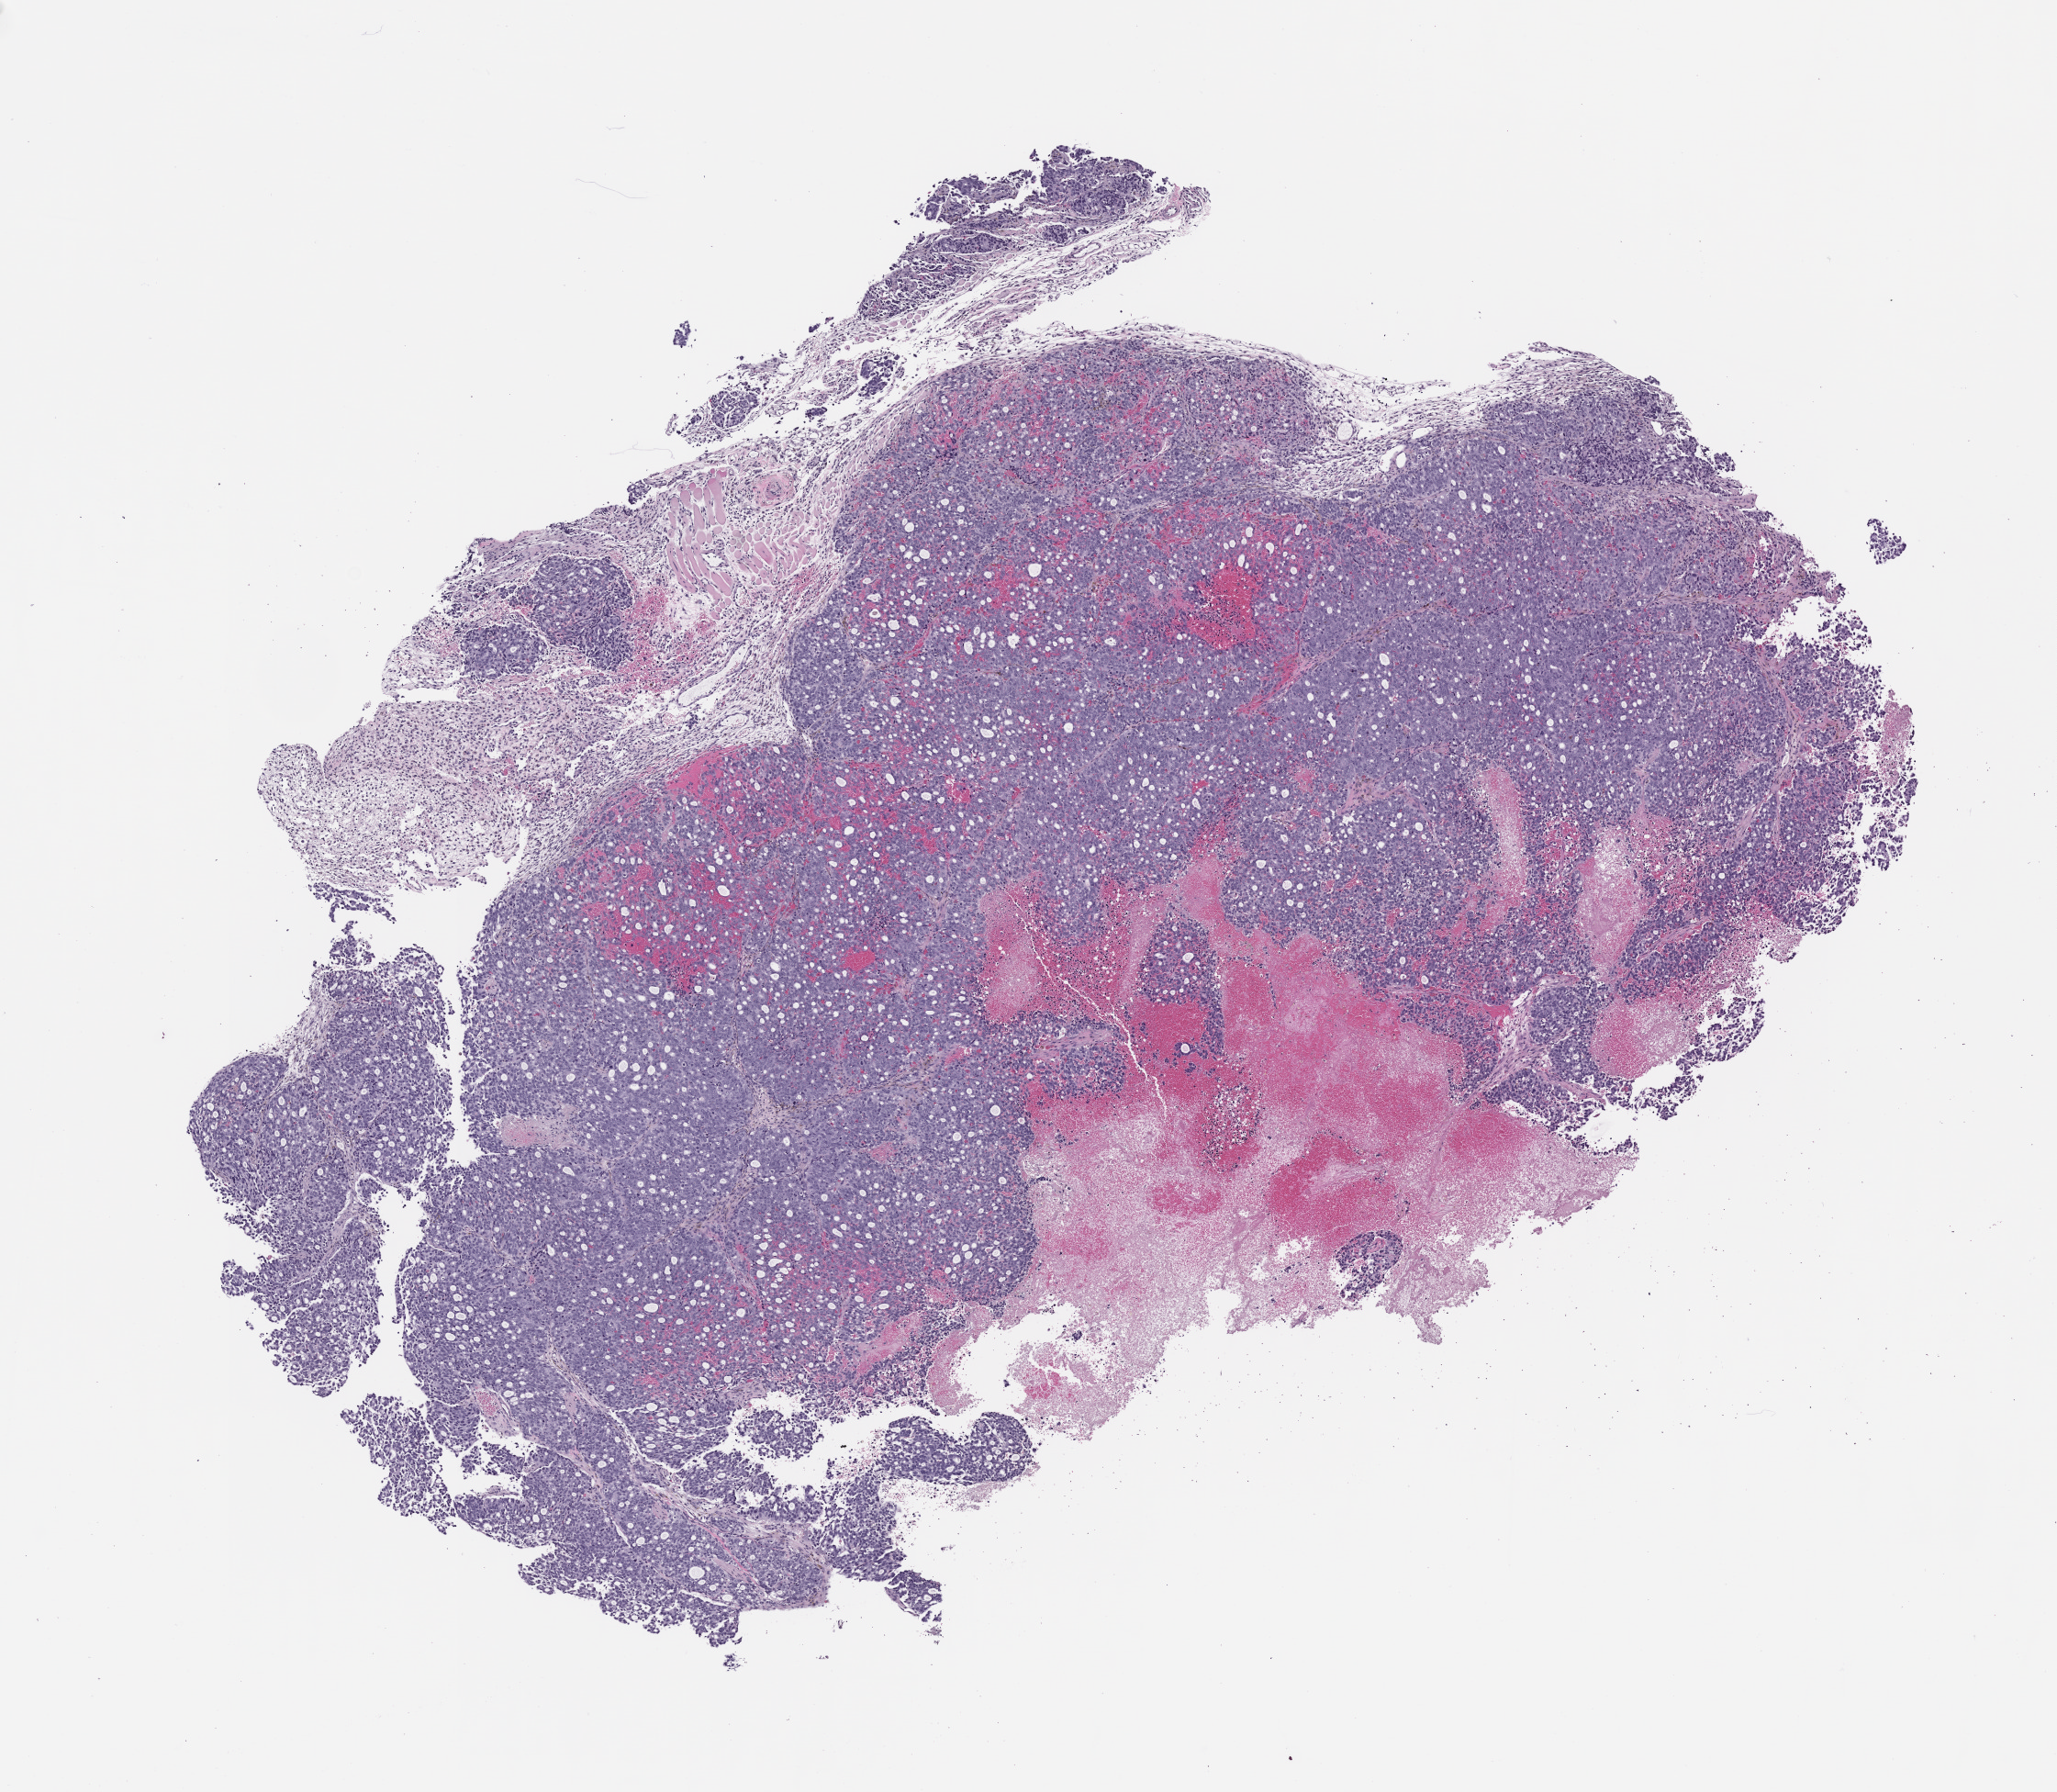
H&E whole-slide image of a patient-derived xenograft (PDX) tumor grown in a mouse — shown as a low-resolution overview of the whole scanned area (about 9.0 x 7.9 mm); FFPE section; originating tumor site category: prostate.
• originating patient diagnosis: Prostate Carcinoma